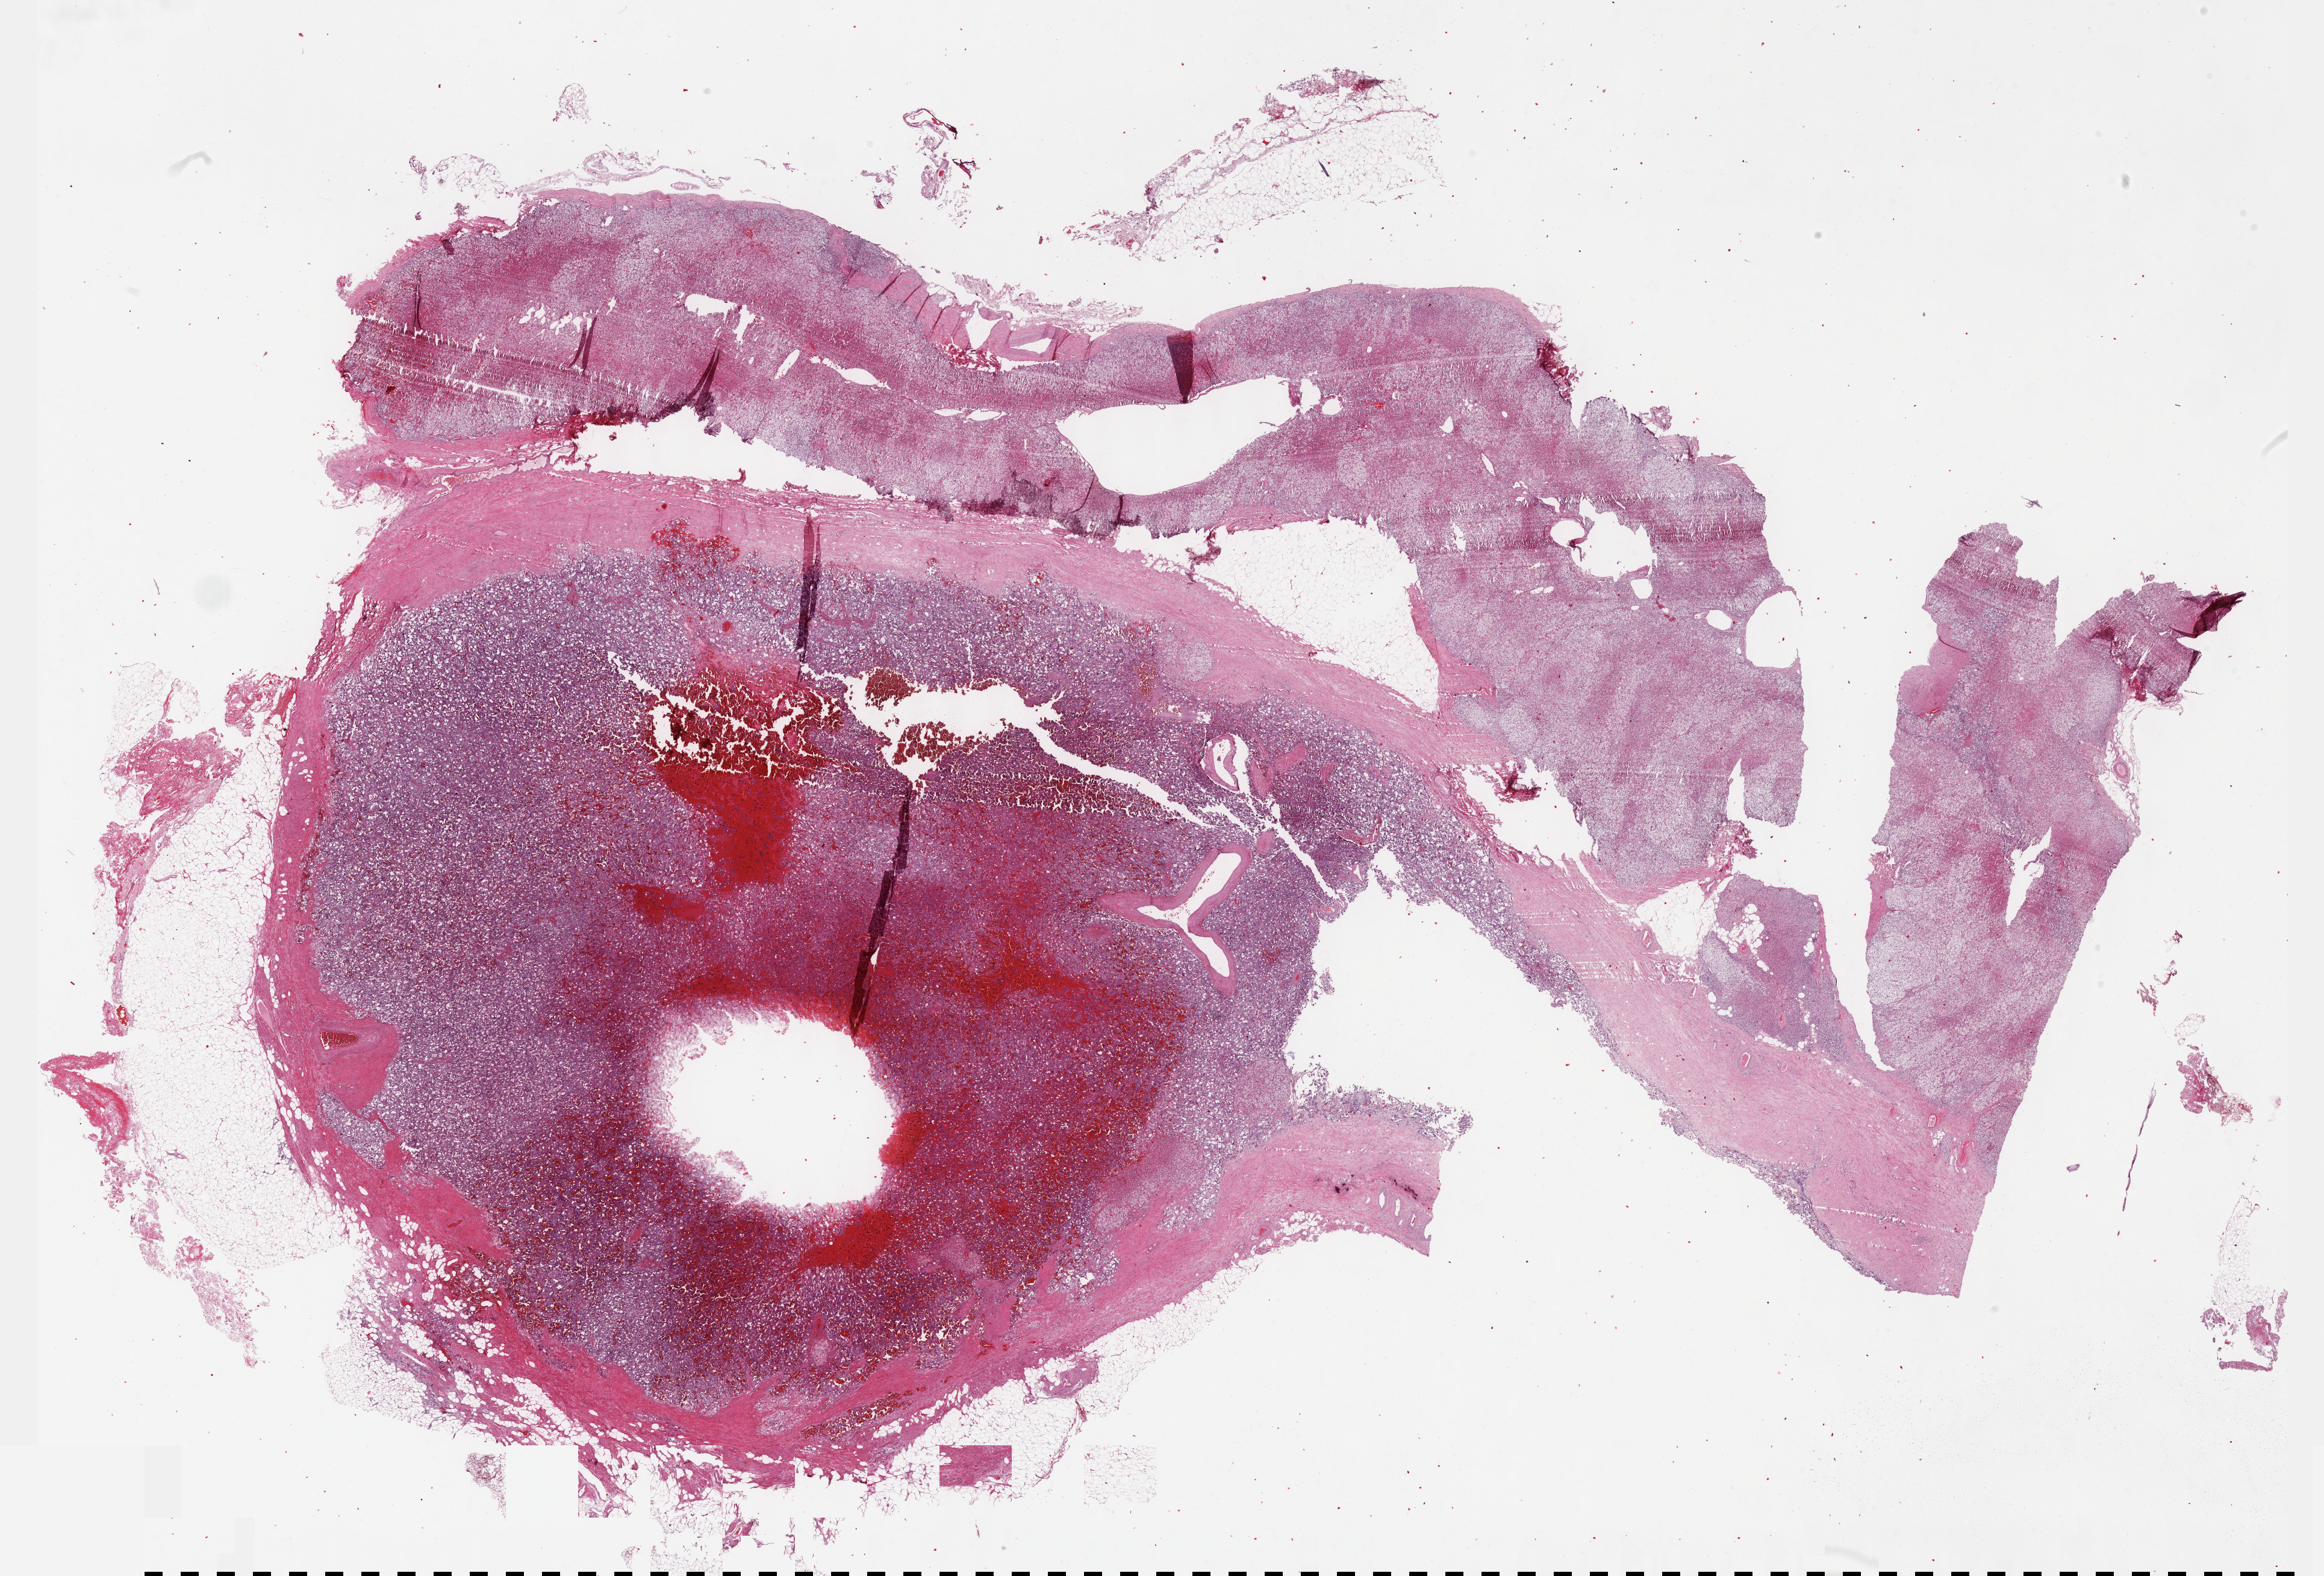
Whole-slide histology image, H&E-stained — whole scanned area (about 31.2 x 21.1 mm) shown as a low-resolution overview; formalin-fixed paraffin-embedded (FFPE) diagnostic section; sample: primary tumour, adrenal gland. Female patient; age at initial diagnosis 83 years.
* pathologic diagnosis: Pheochromocytoma, NOS
* laterality: left